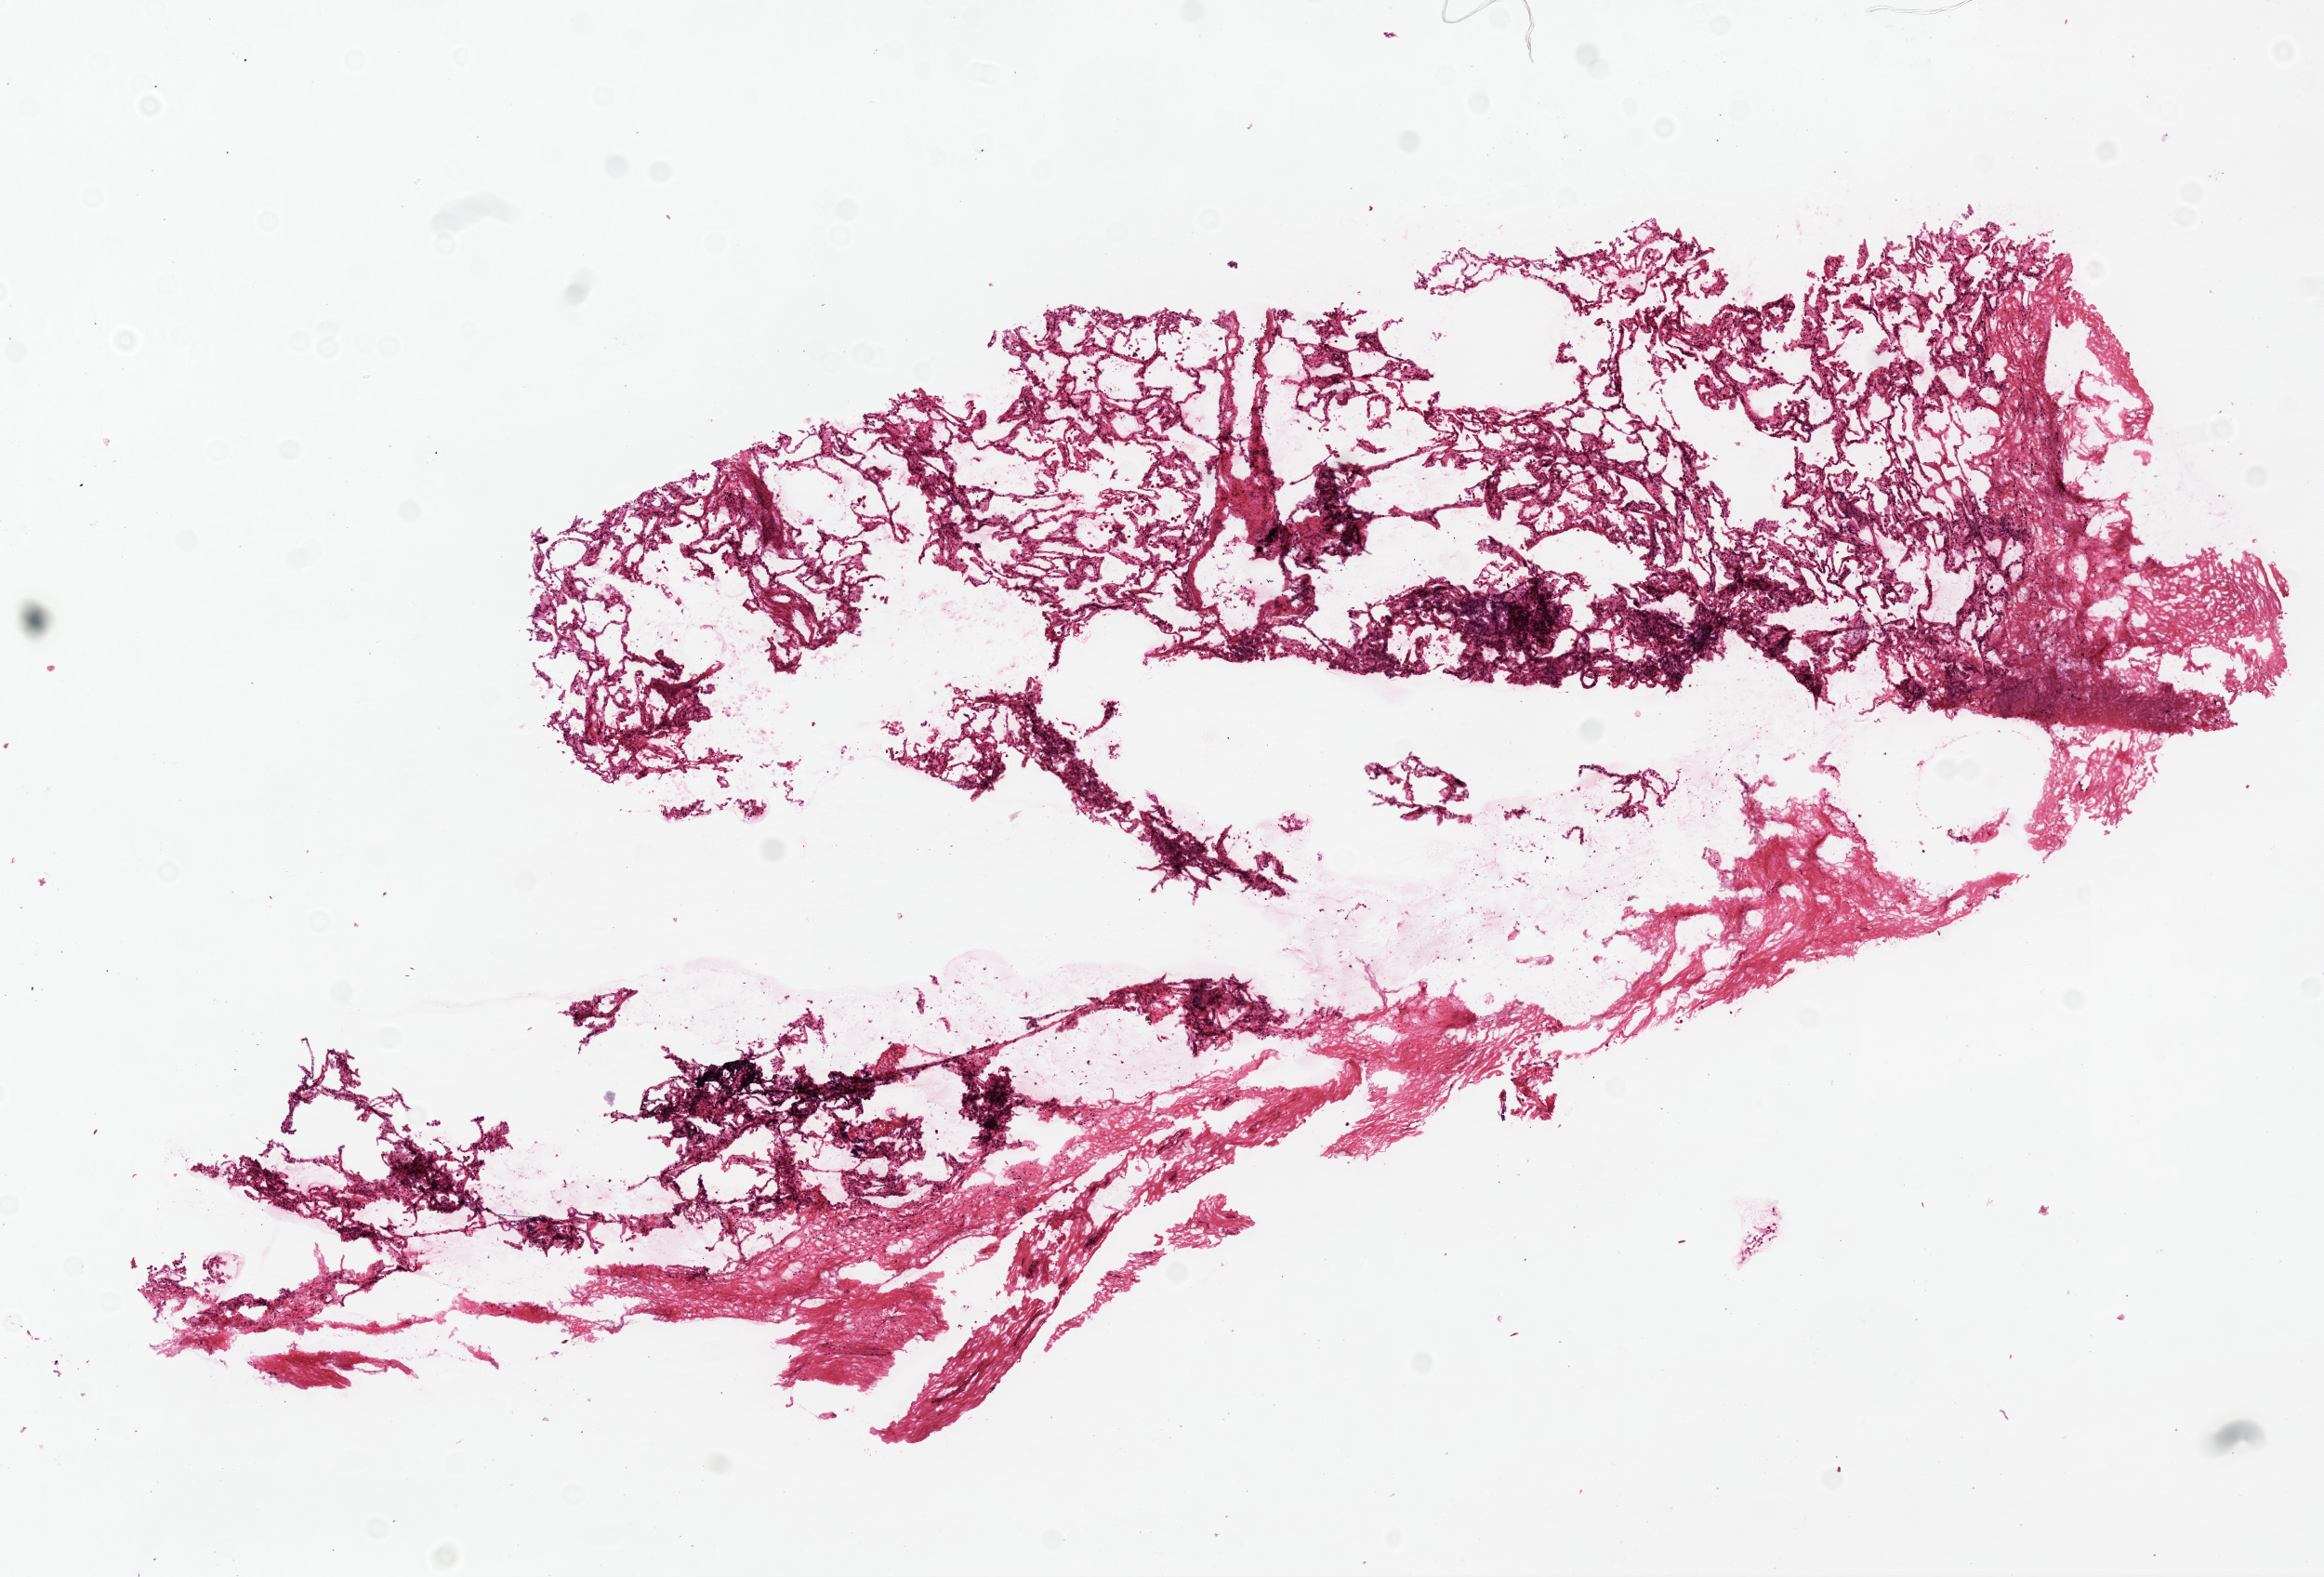
Hematoxylin and eosin (H&E) stained whole-slide image, a low-resolution overview of the entire scanned area, about 10.0 x 6.8 mm (from a 20x scan); frozen section from the top of the tissue portion; sample: solid tissue normal (non-tumour tissue), lung. Patient: male, age at initial diagnosis 76 years.
• this section: solid tissue normal sample (biorepository sample class)
• patient diagnosis: Squamous cell carcinoma, NOS (upper lobe, lung)